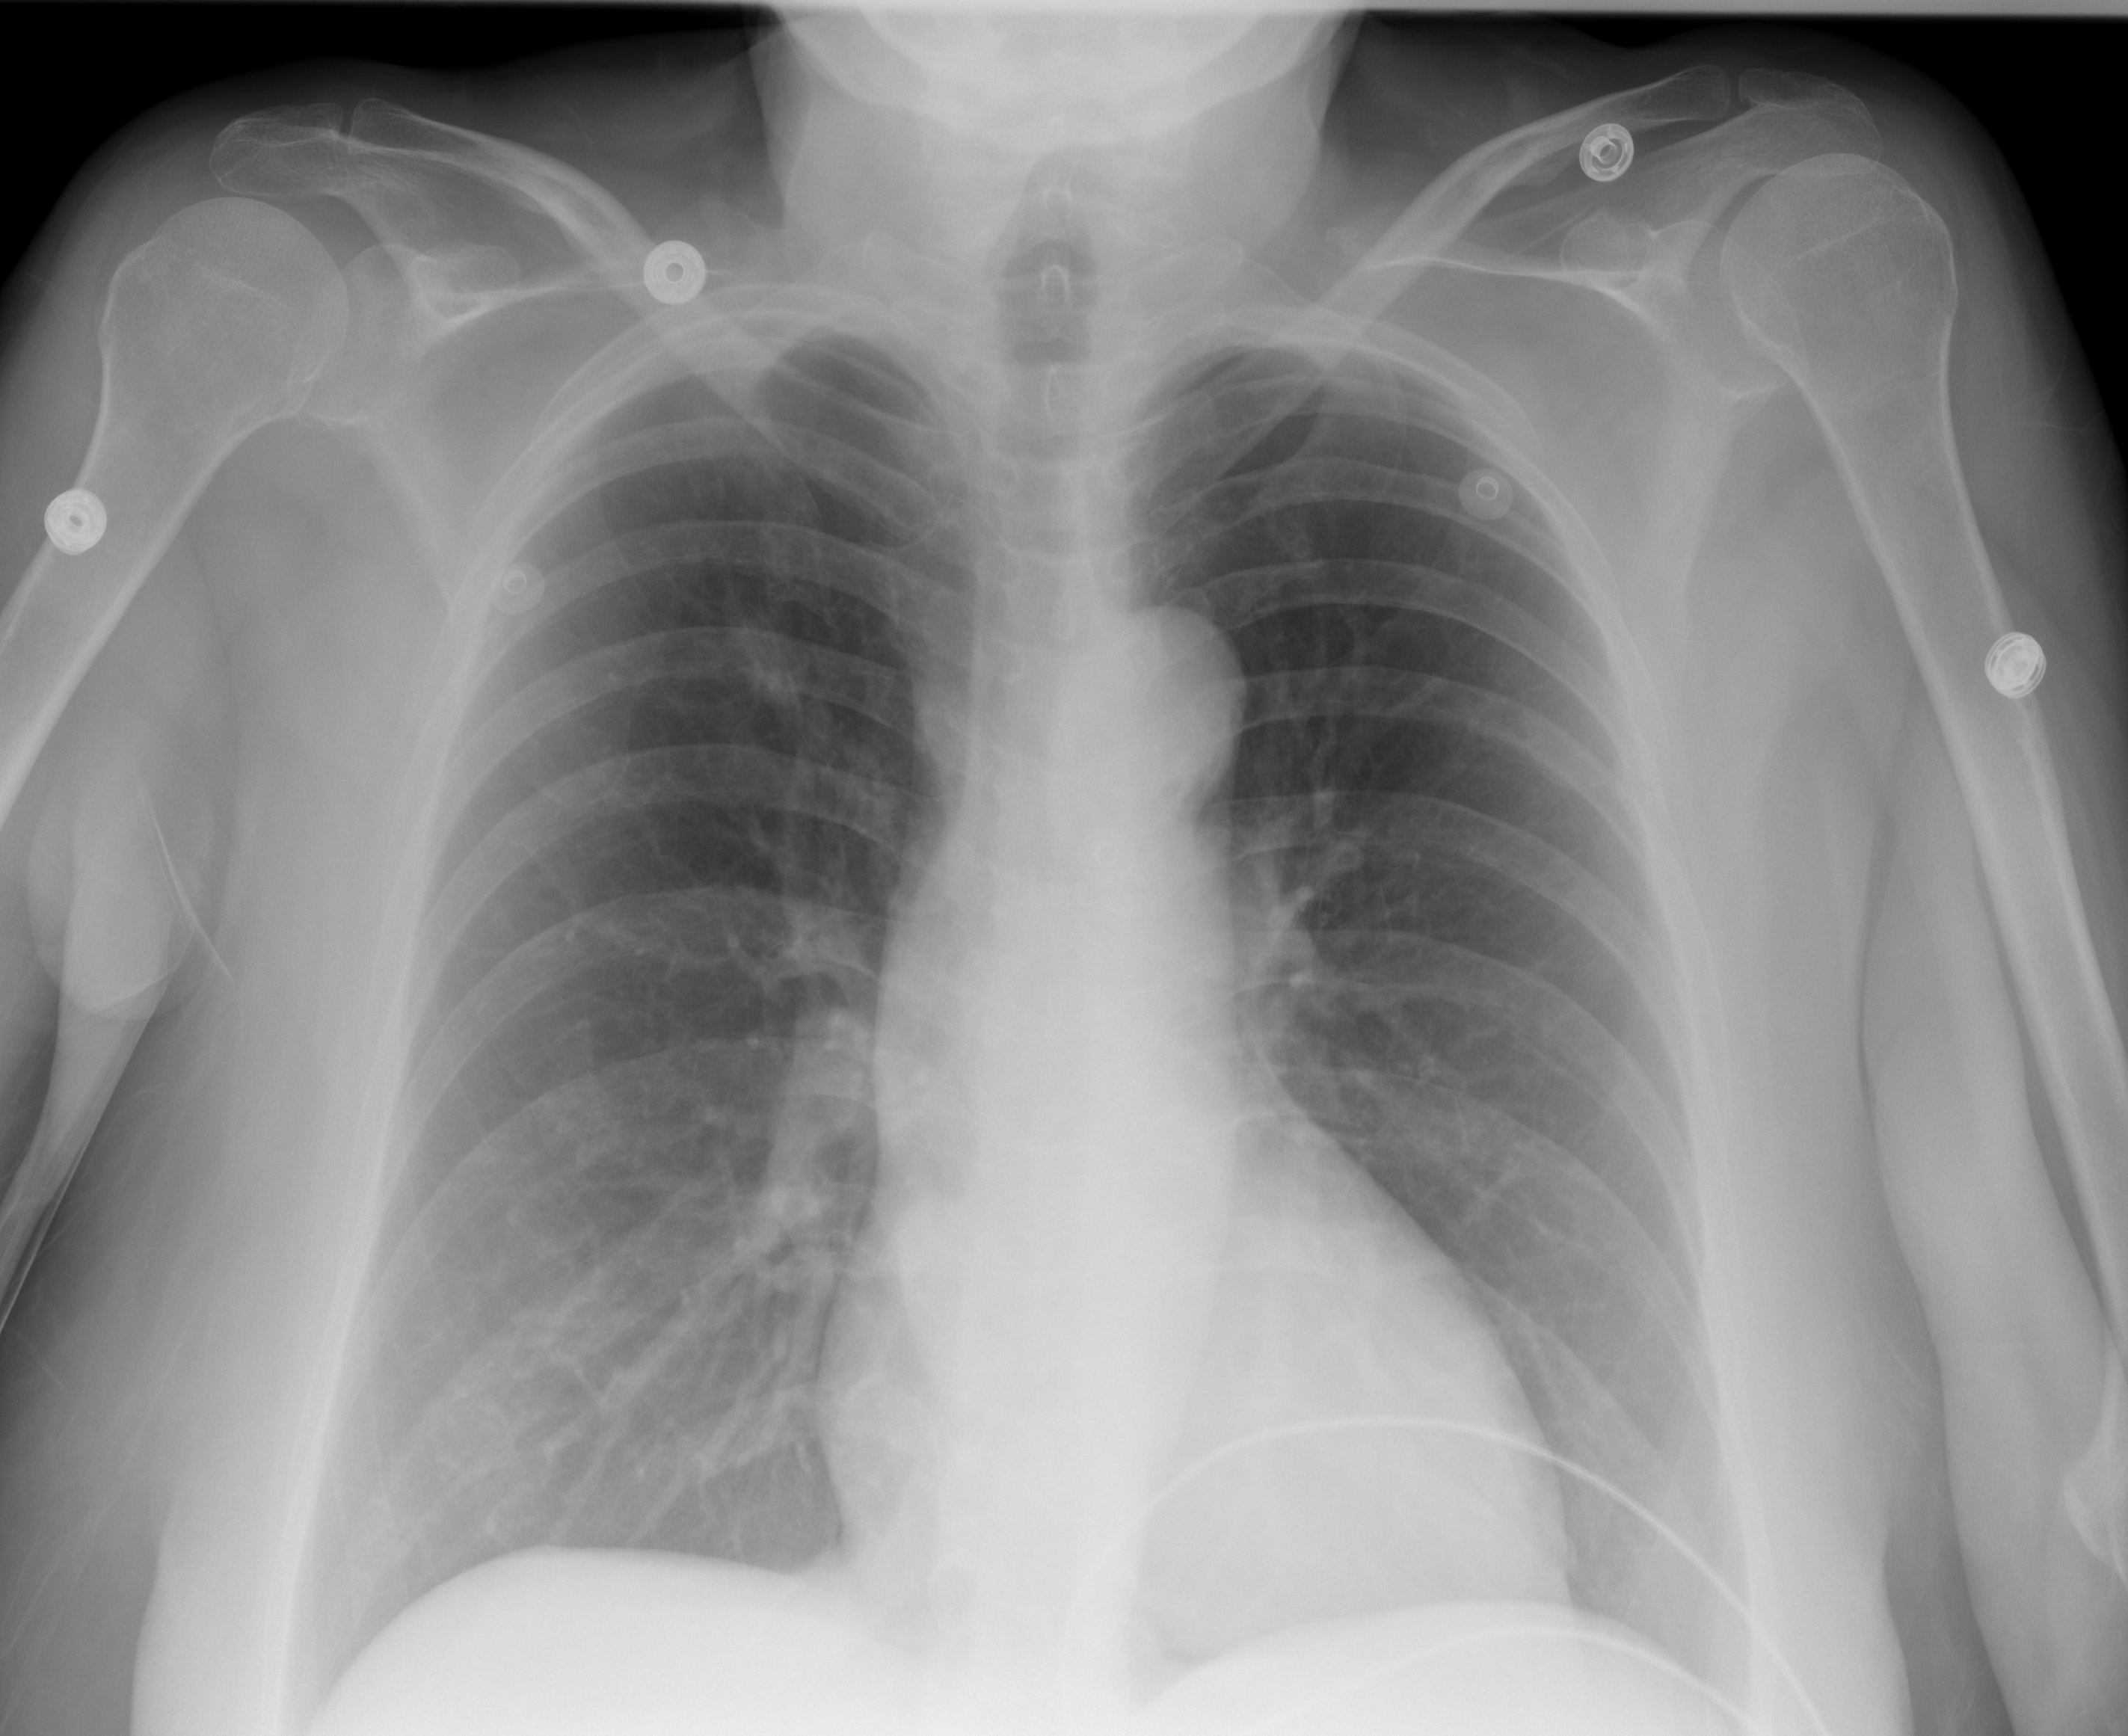
Portable chest radiograph, AP projection. Female patient, age 59 years; imaged 22 days after the COVID-19 diagnosis.
Radiologist's key findings for this exam: No significant pleural effusions. No acute consolidation.